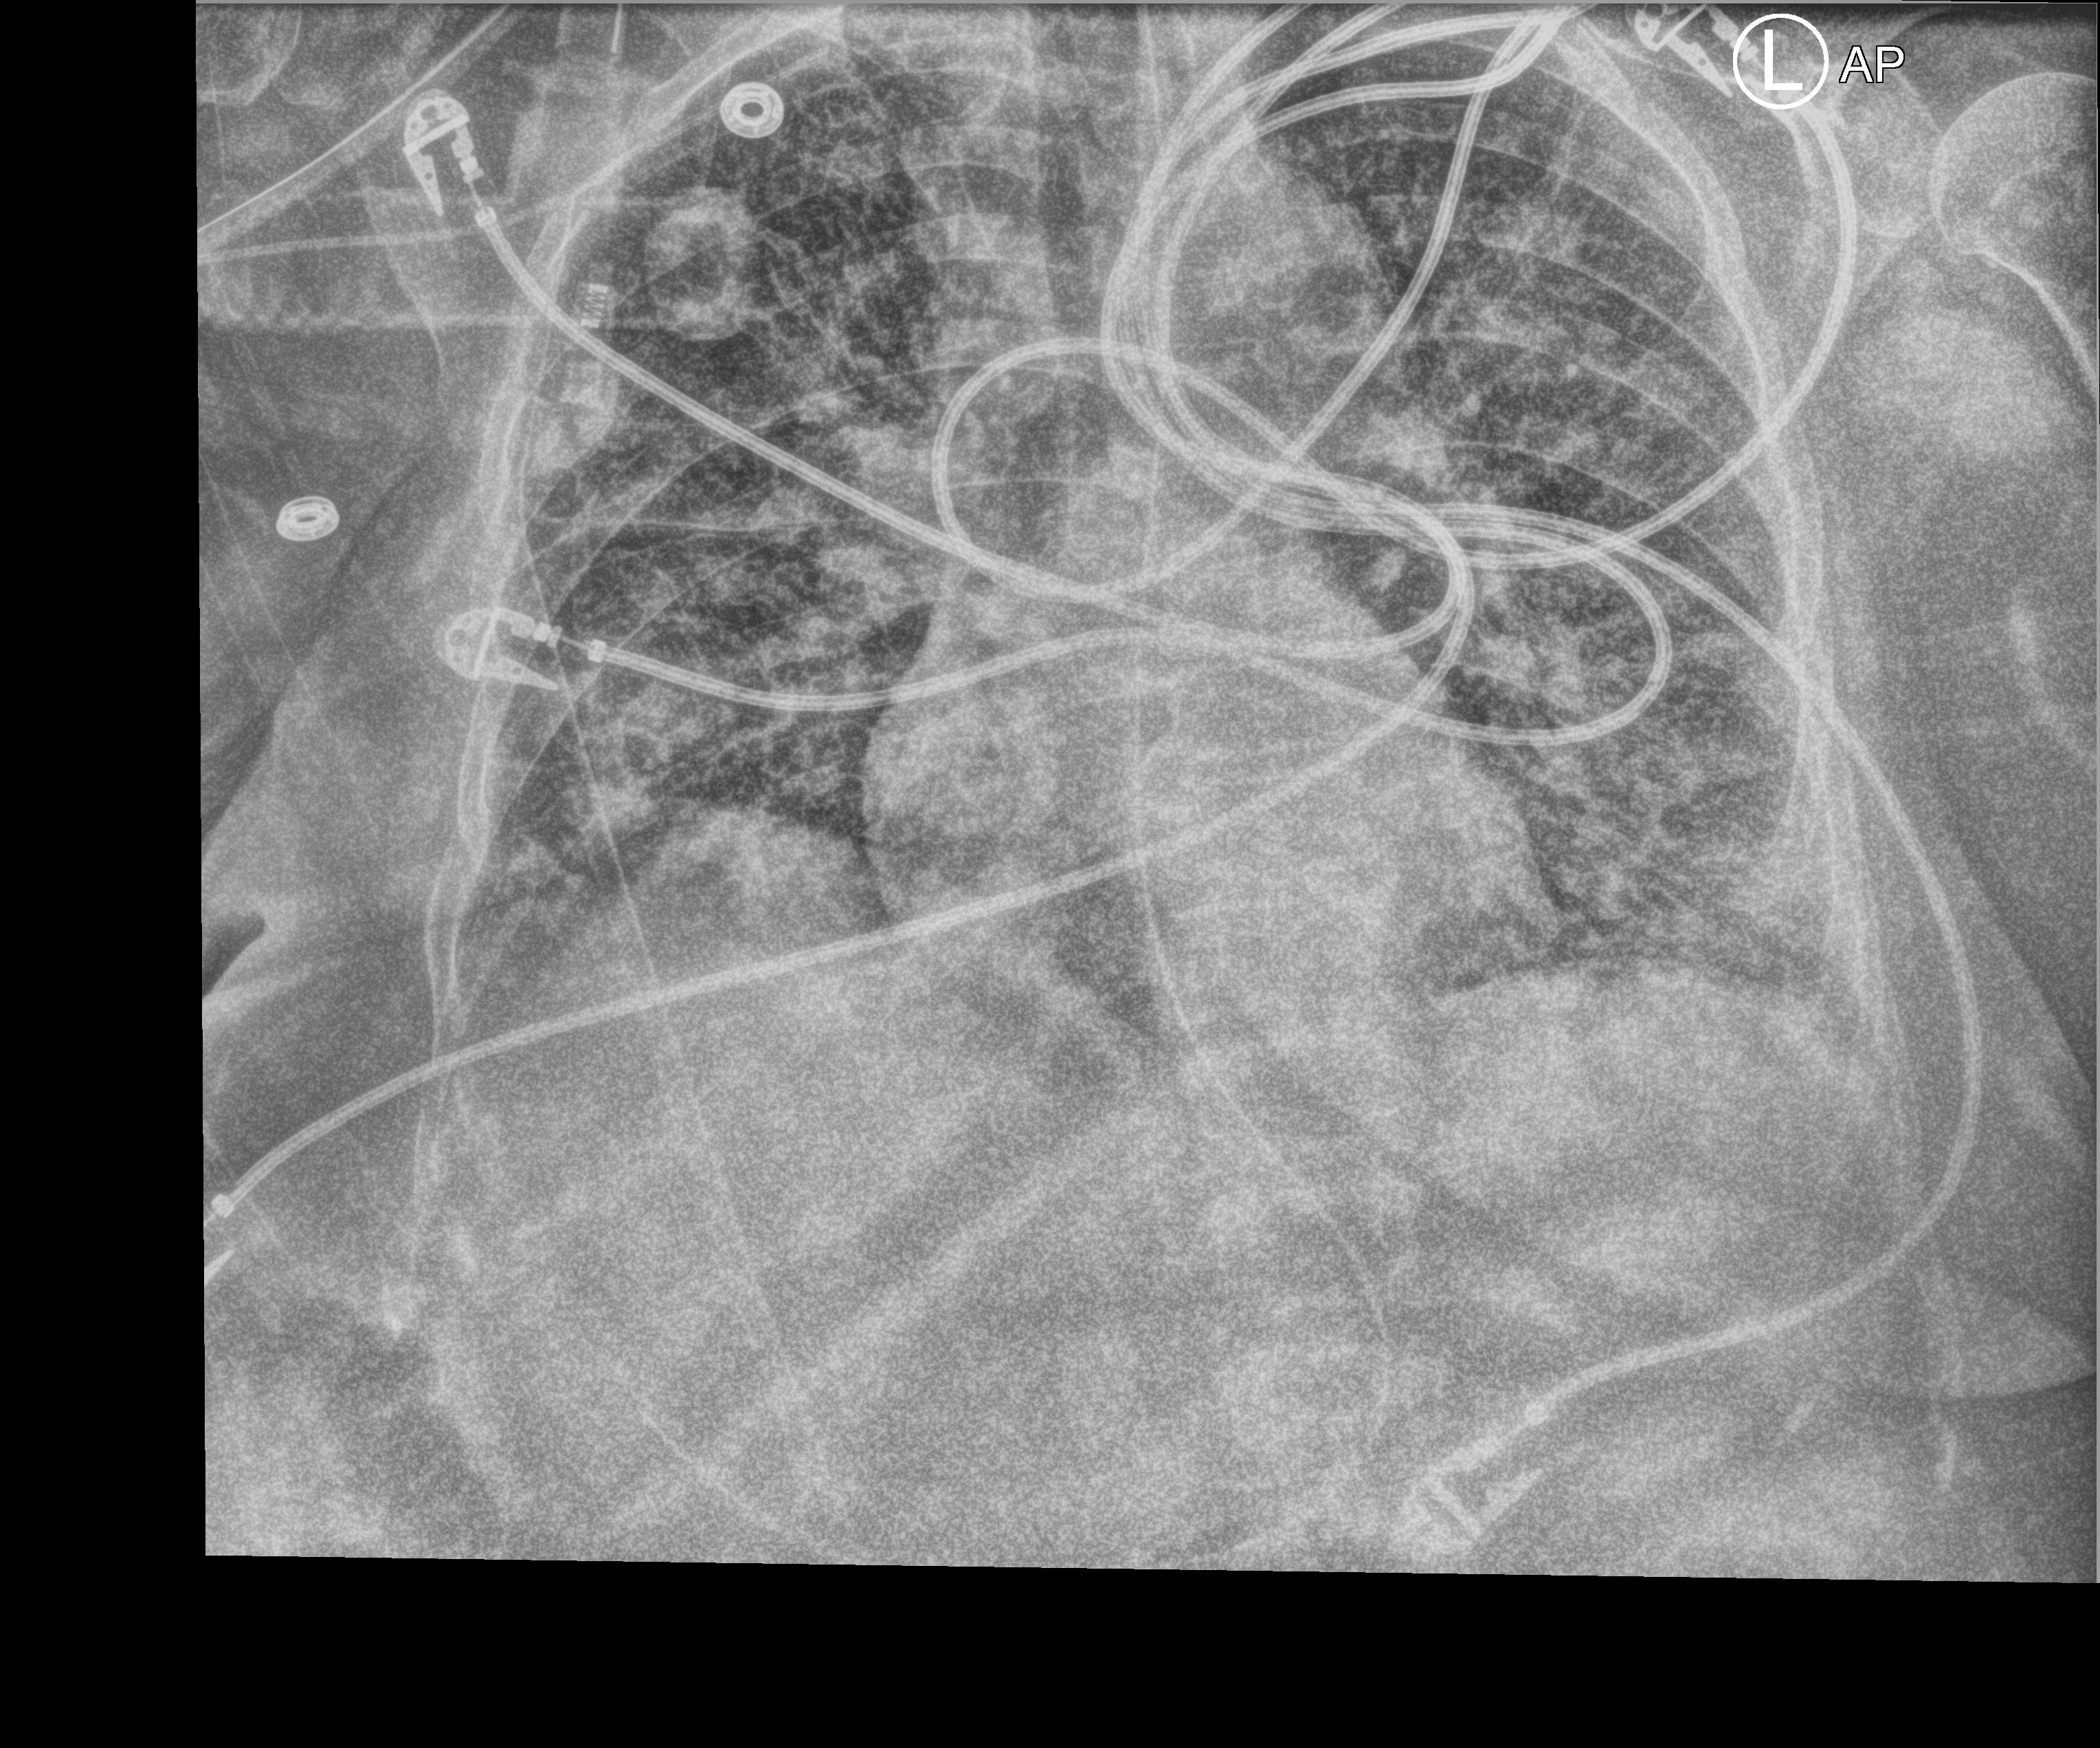
Bedside chest radiograph (computed radiography); anteroposterior (AP) projection. Female patient hospitalised with COVID-19, age 60–74 years.
Hospital-stay facts (about this admission, not read from this image; timing relative to this image not recorded): COPD (admission record): no; other chronic lung disease (admission record): no.